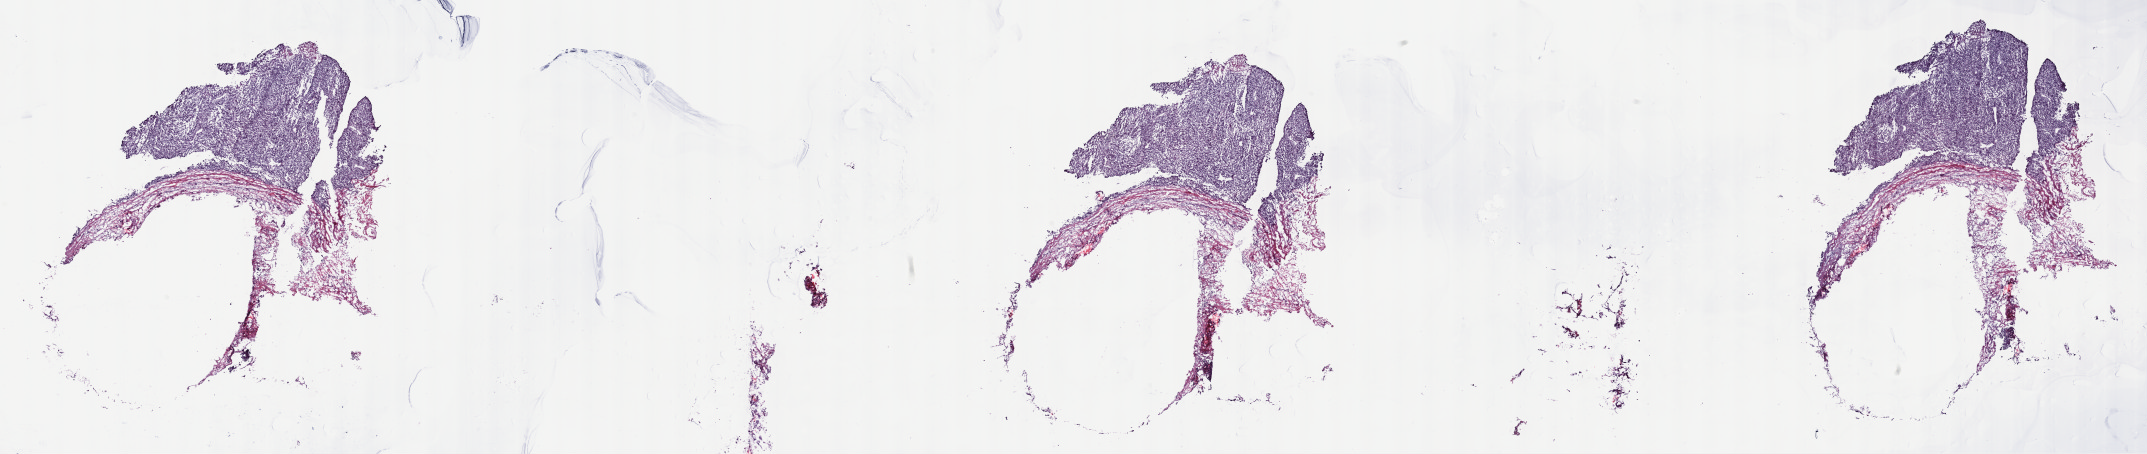
Whole-slide histology image, H&E — shown as a low-resolution overview of the whole scanned area (about 34.7 x 7.3 mm), frozen section from the top of the tissue portion, metastatic tumour sample, sampled site: lymph nodes of inguinal region or leg. Female, age 84 years at initial diagnosis. Composition of this section per pathologist review: tumour cells 70%, tumour nuclei 90%, normal cells 0%, stromal cells 30%, necrosis 0%. Inflammatory infiltration, as recorded: lymphocyte infiltration 0%, monocyte infiltration 0%, neutrophil infiltration 0%.
This section: metastatic tumour tissue. Patient diagnosis: Malignant melanoma, NOS.